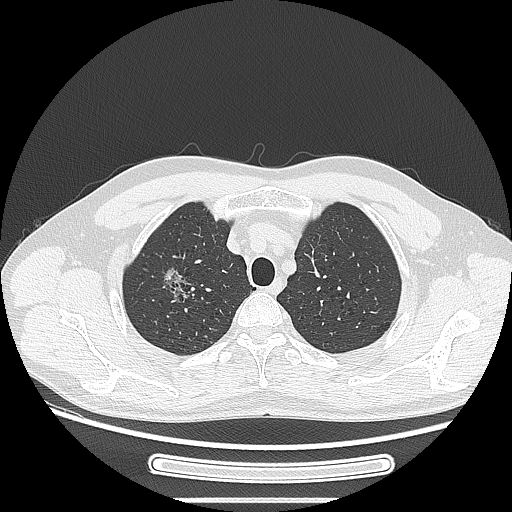
Chest CT, one axial slice; position 219 of 269 along the scan axis; 120 kVp; lung window (W 1500 / L -600 HU); 512 × 512 image matrix, field of view 382 × 382 mm. Male patient, age 53 years. Case-level facts recorded for this patient, not image findings: clinical TNM (as recorded): T1c N0 M0; histopathological grade: G2.
Structures marked on this image (bounding box drawn by a radiologist):
- lung tumour (recorded histology: adenocarcinoma): box from (x=151, y=256) to (x=195, y=313) px